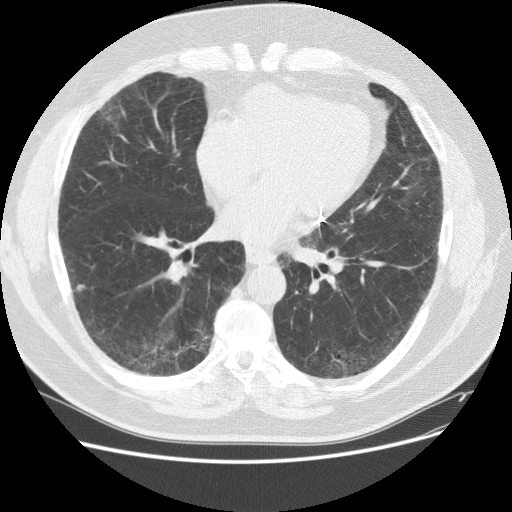
Low-dose screening chest CT, one axial slice; slice 73 of 151 in the series (ordered by position); reconstruction kernel STANDARD; 120 kVp; lung window (W 1500 / L -600 HU); 2.5 mm slice thickness; 512 × 512 image matrix.
Annotated regions visible in this slice (manually delineated by an expert):
- lesion 1 (tumor, lower lobe of right lung): bounding box [x1, y1, x2, y2] px = [77, 284, 86, 293]